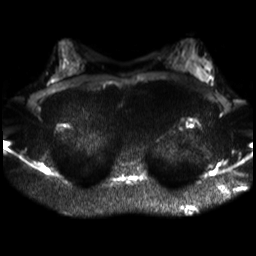
Breast MRI, one axial slice. Slice 18 of 30 in the series (ordered by position). Diffusion-weighted series; image 2 of 4 stored at this slice position (different b-values; order by instance number). 3 T. 4 mm slice thickness. 256 × 256 image matrix, field of view 320 × 320 mm. Female patient.
Structures marked on this image (expert manual segmentation):
- tumour on diffusion-weighted imaging: bounding box <202,72,206,76> (left, top, right, bottom; pixels)